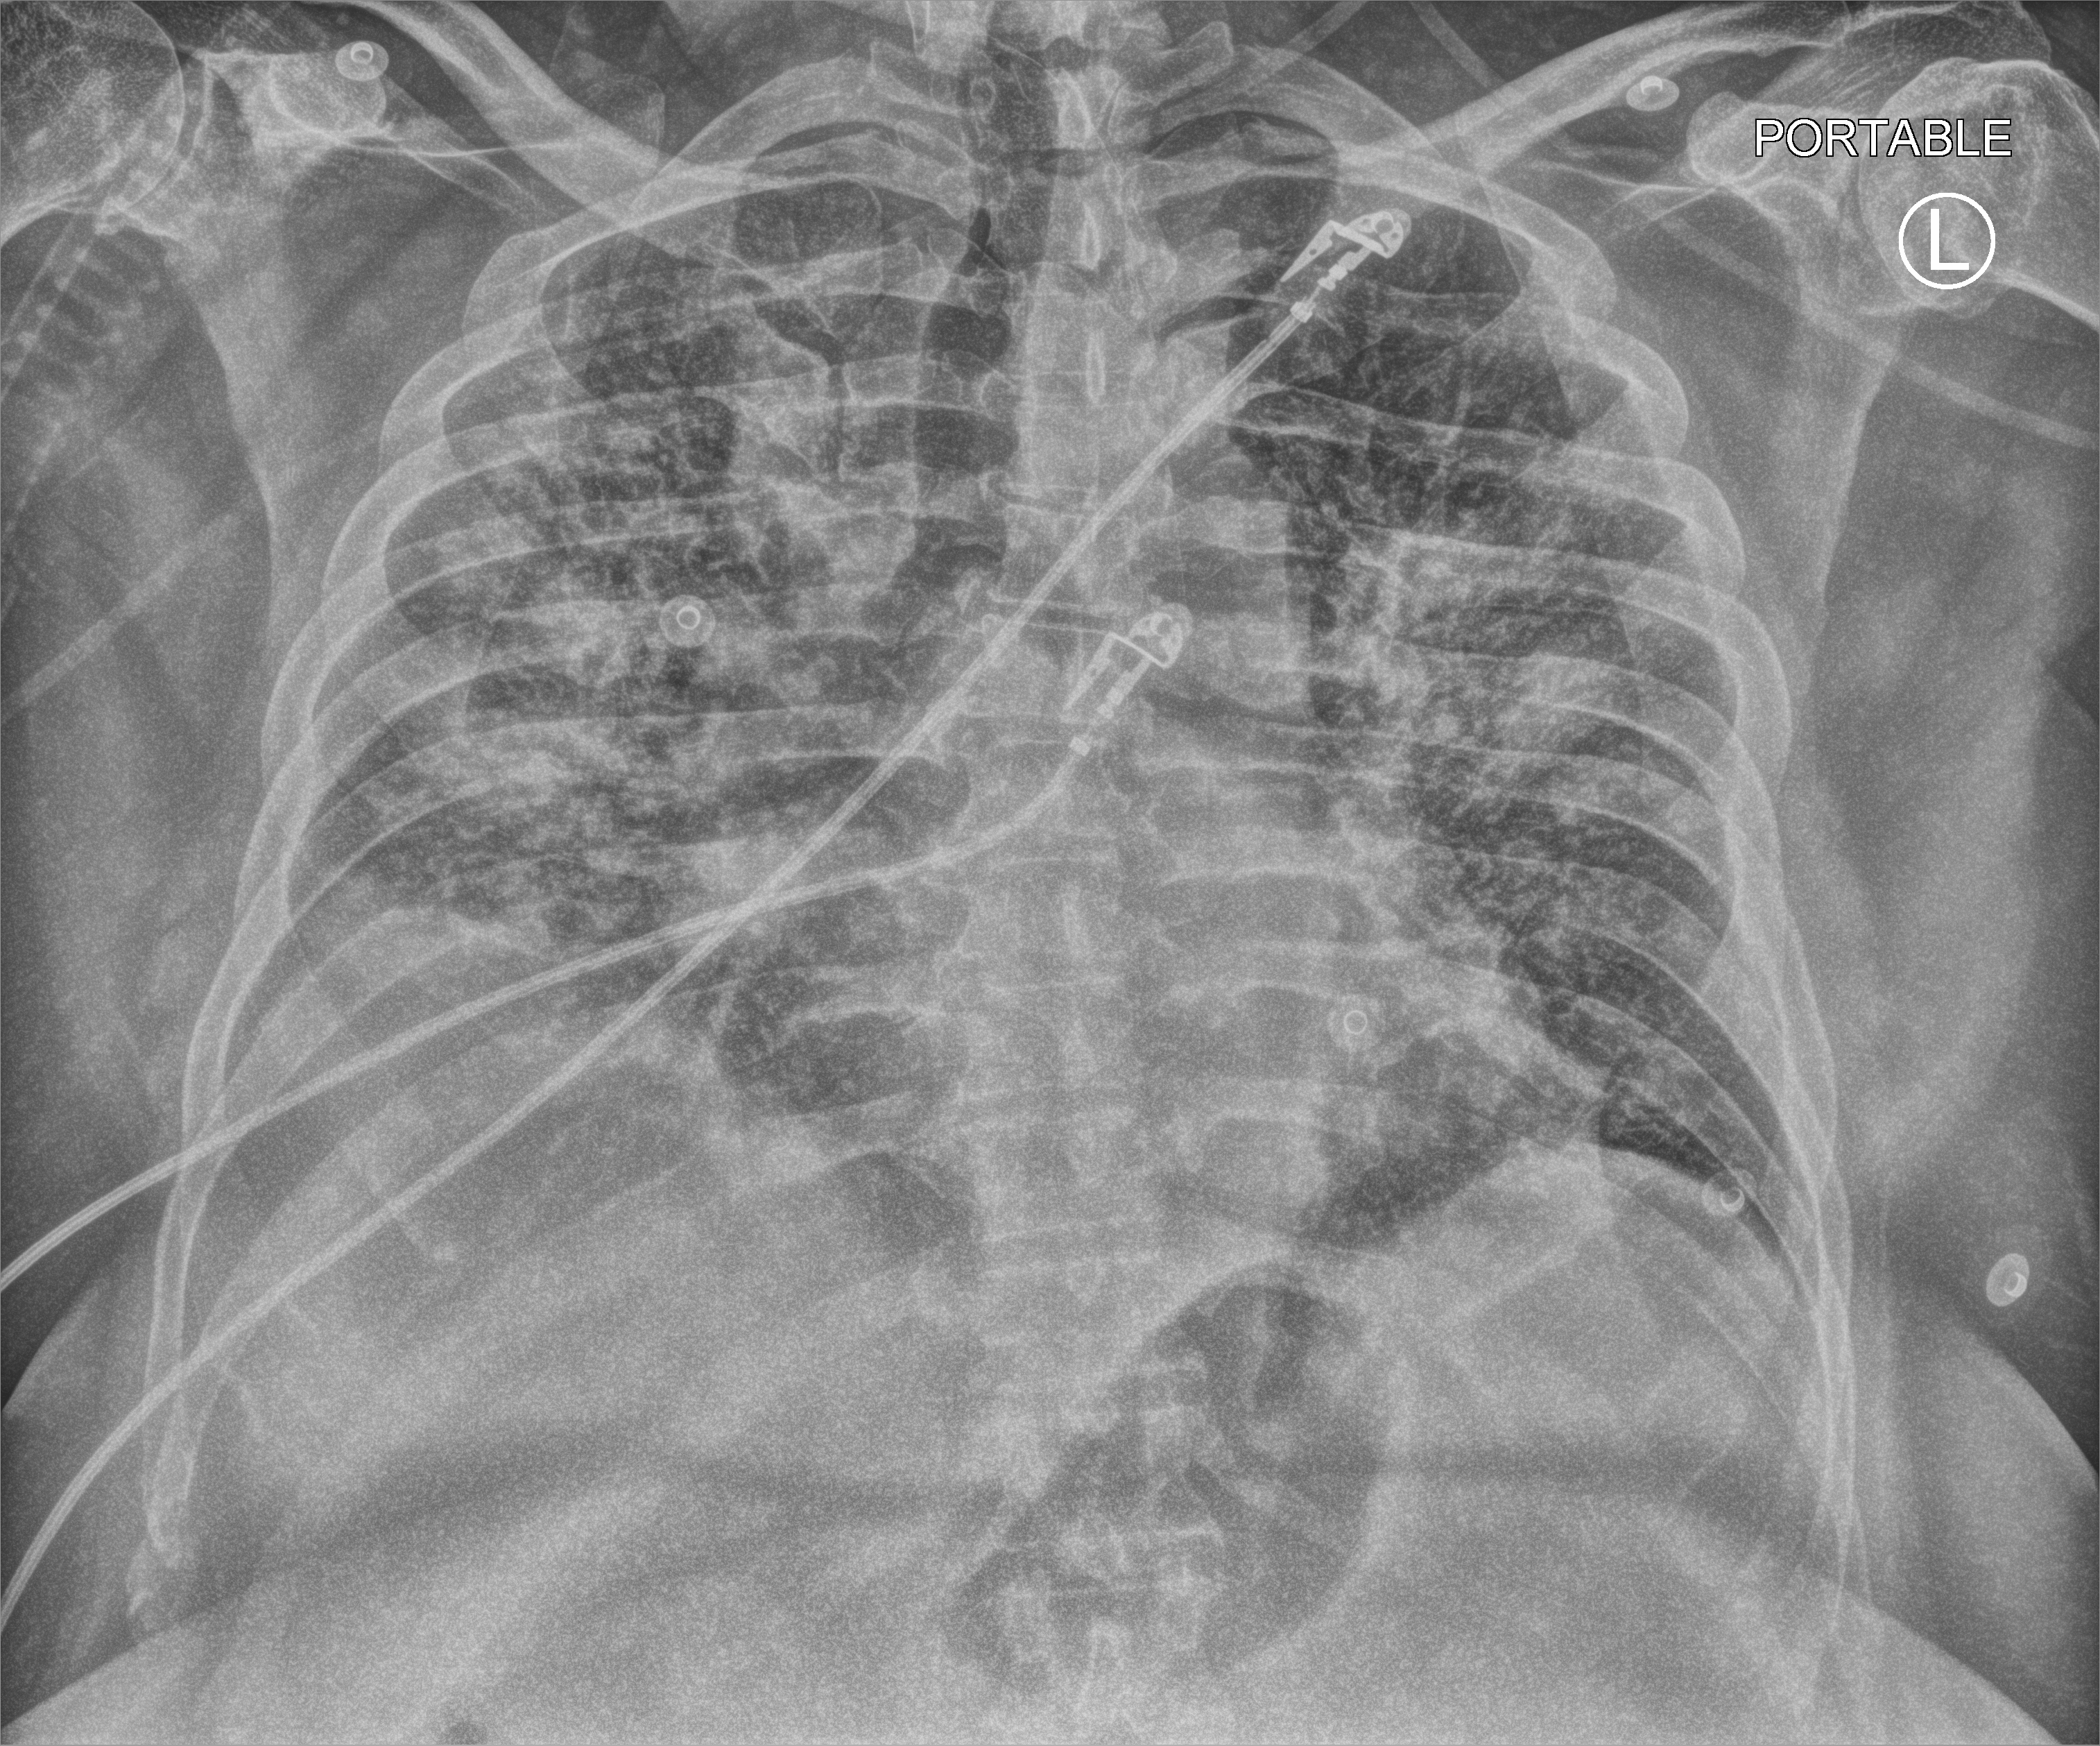
Chest X-ray (portable), anteroposterior (AP) projection. Male patient hospitalised with COVID-19, age 18–59 years.
From the hospital-stay record, not from the radiograph (when in the stay this image was taken is not recorded):
- smoking status (admission record): never
- hypertension (admission record): yes
- COPD (admission record): no